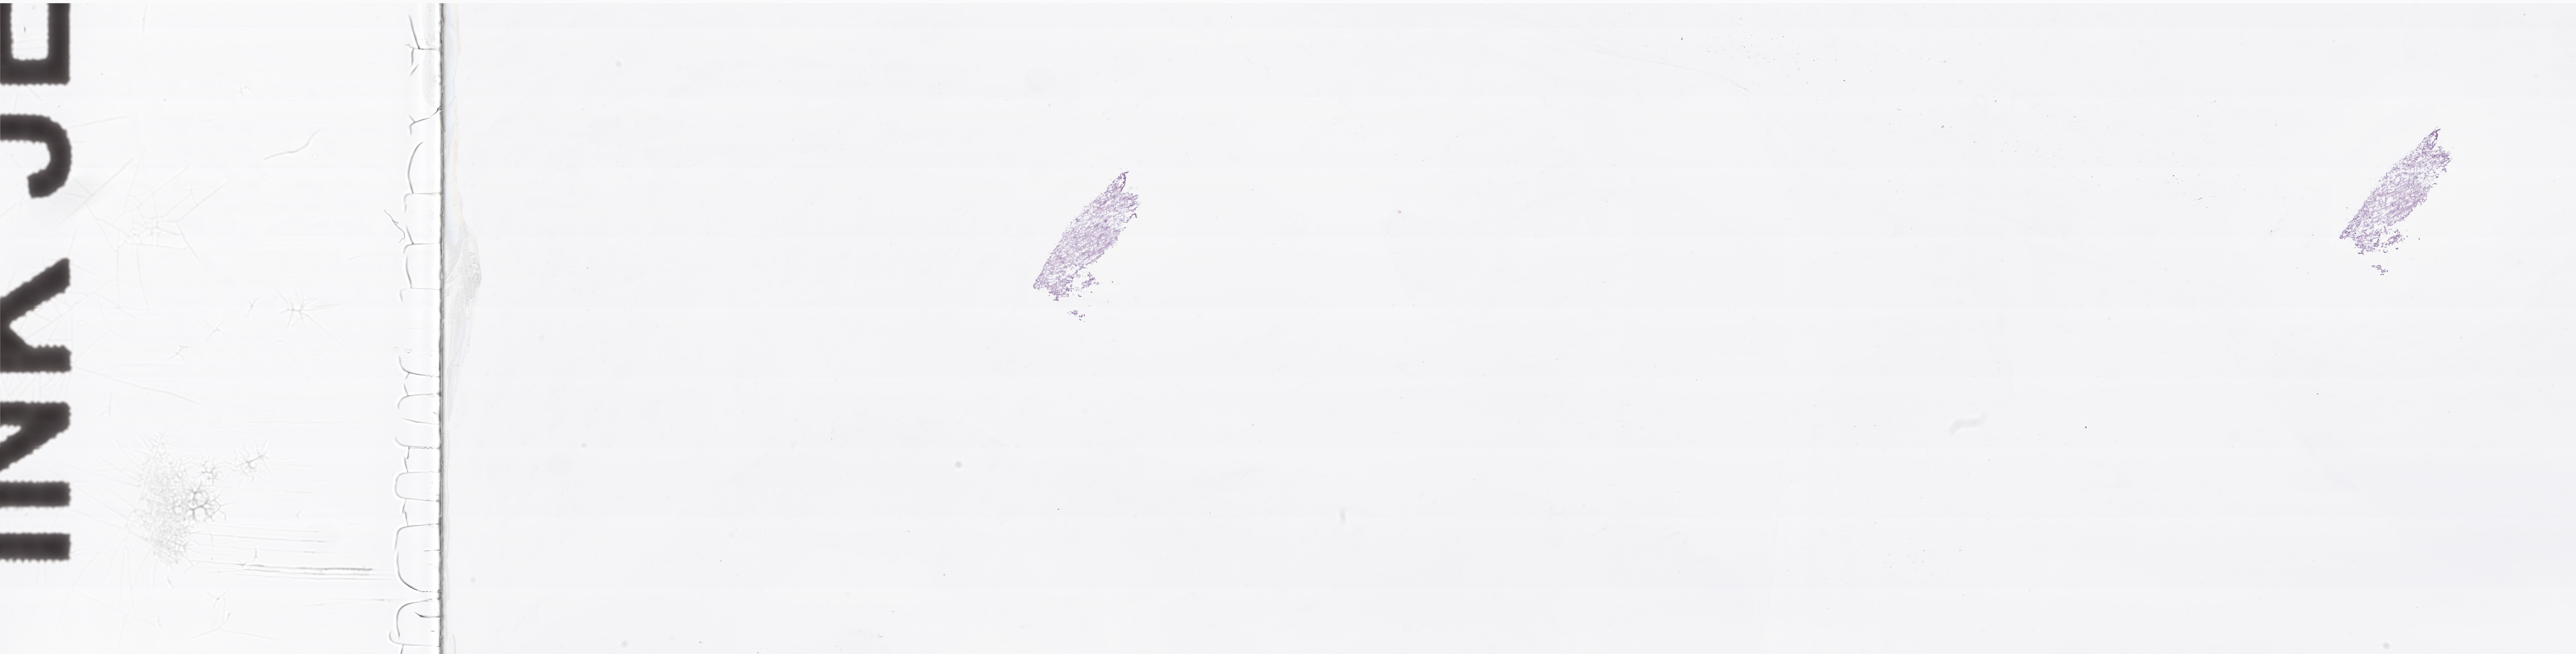
Digitized H&E-stained section of tumor tissue from the brain — whole scanned area (about 39.3 x 10.0 mm) shown as a low-resolution overview. Cryosection (OCT / tissue freezing medium). Patient: male, age 42 months (3 years 6 months).
Diagnosis (ICD-O-3 morphology term): Pilocytic astrocytoma.